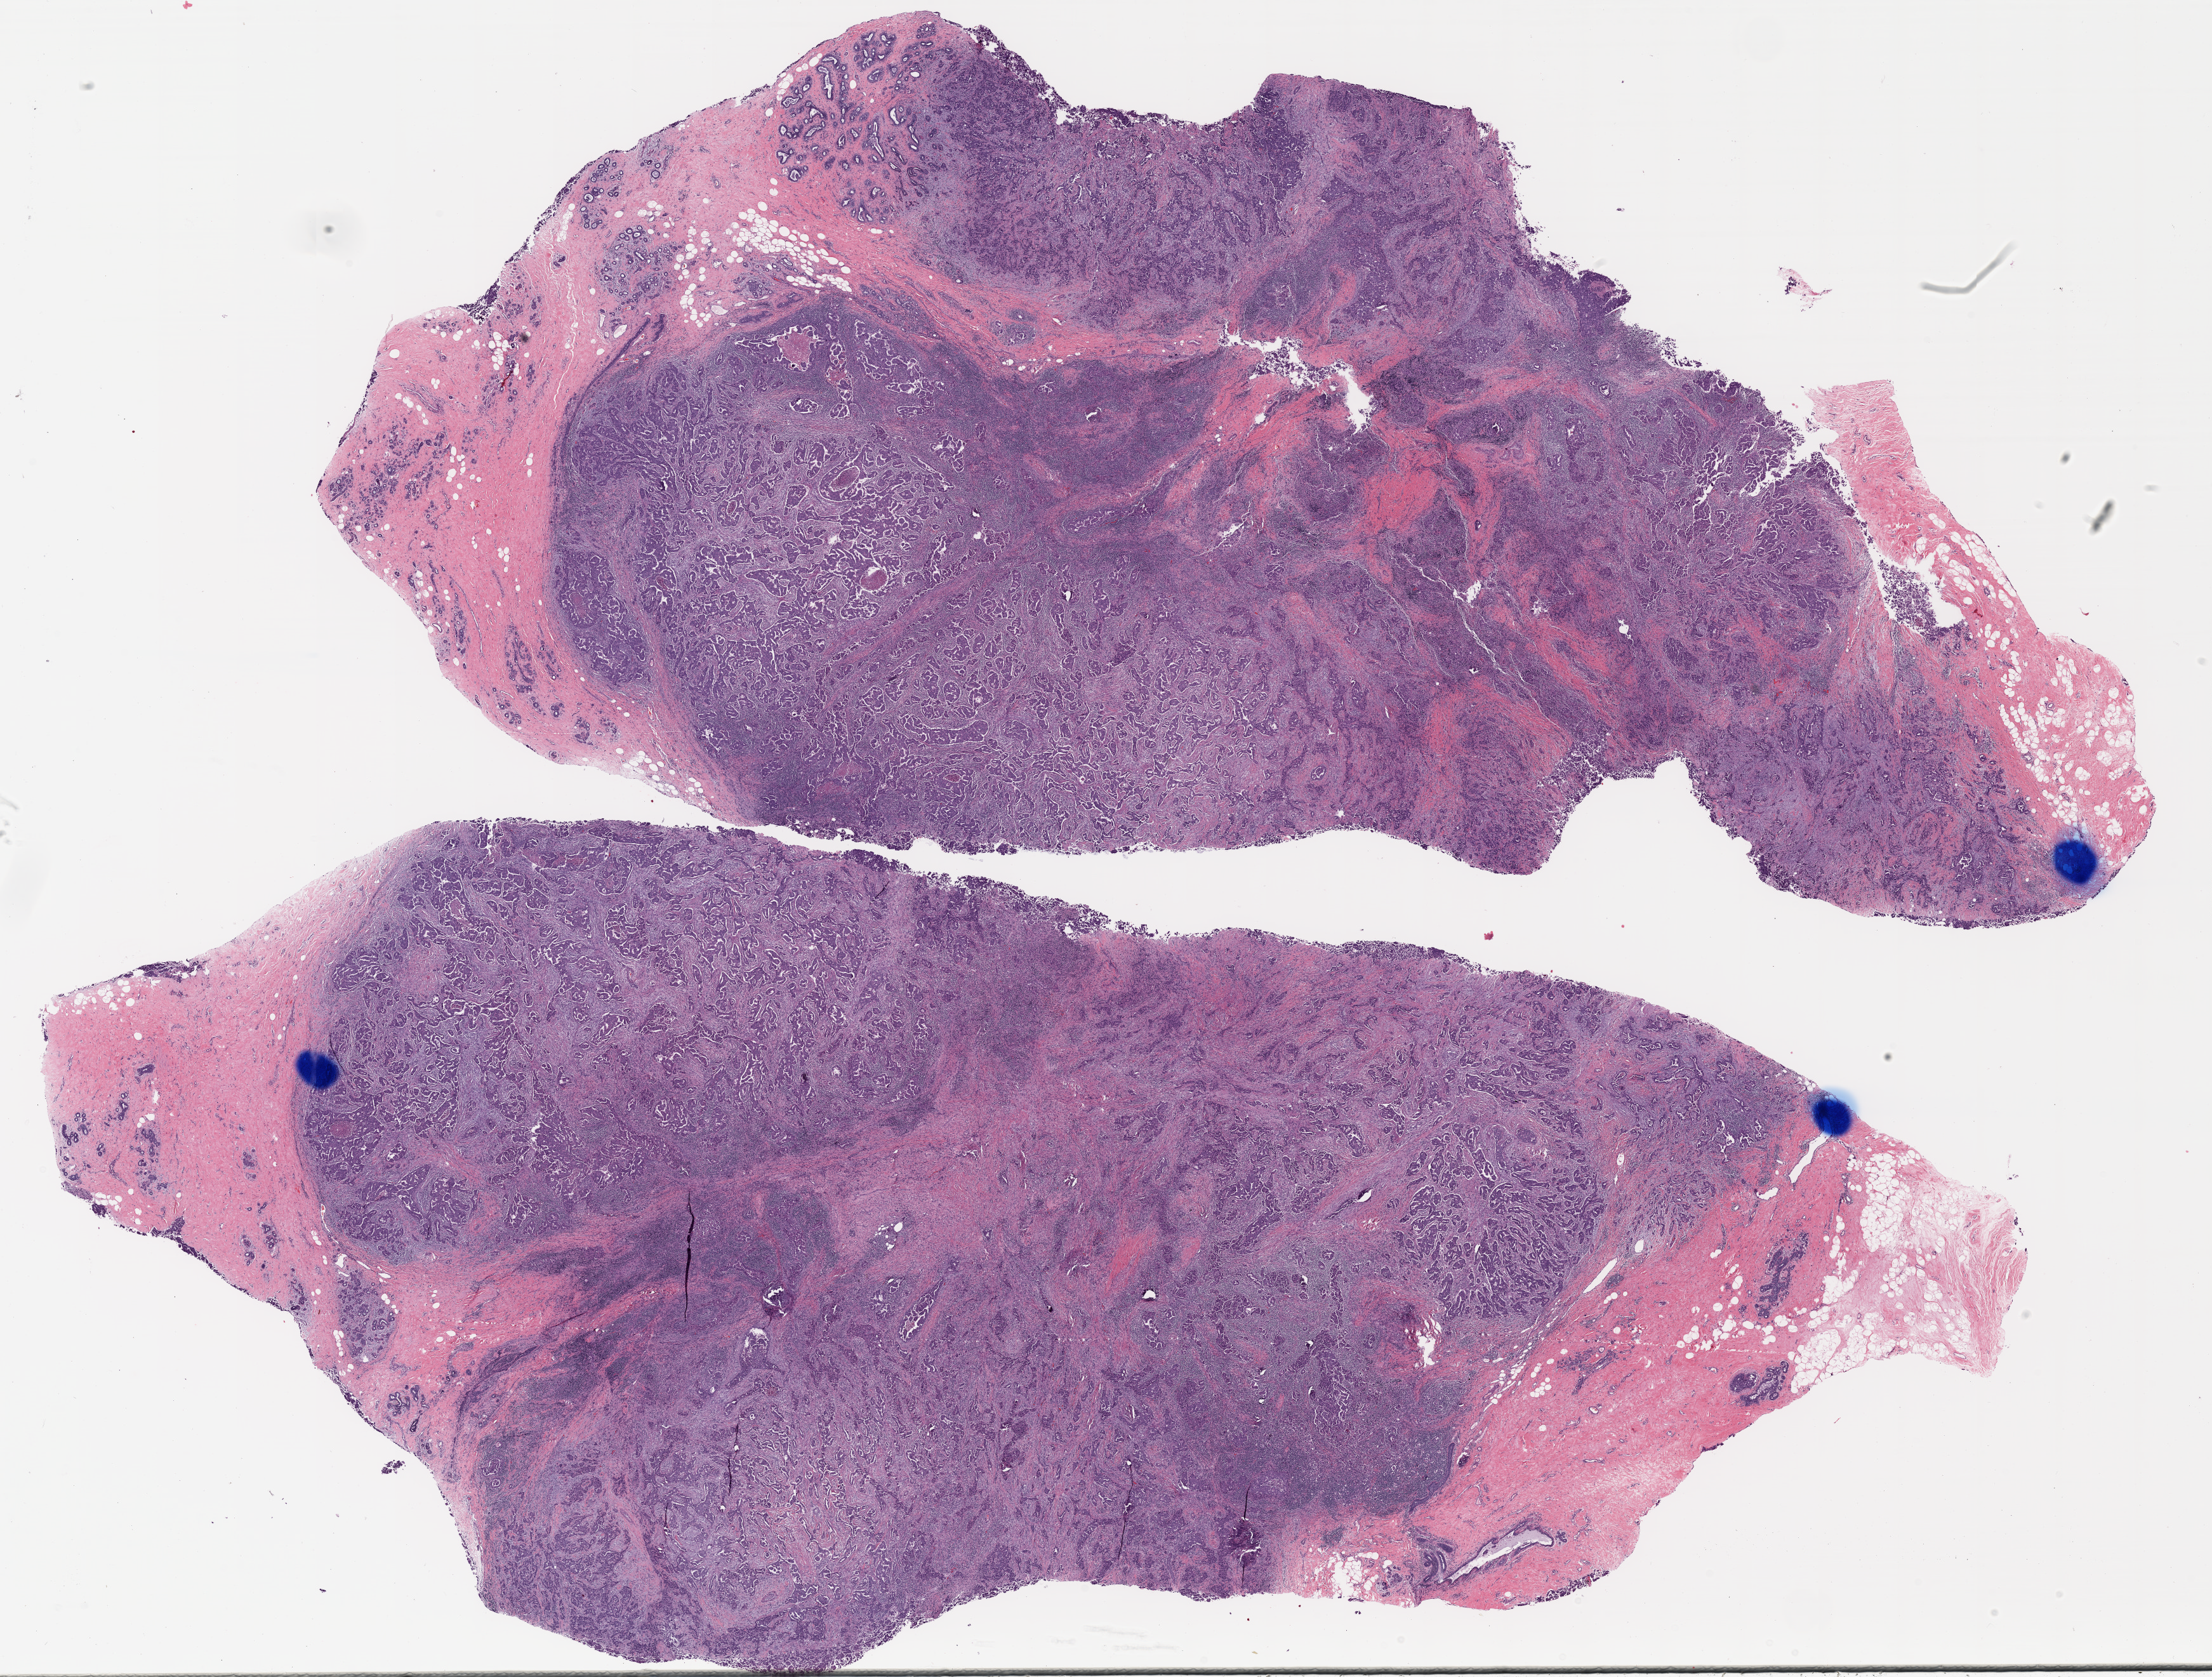
Digitized Hematoxylin and eosin (H&E) stained tissue section (whole slide), shown as a low-resolution overview of the whole scanned area (about 27.8 x 21.1 mm), formalin-fixed paraffin-embedded (FFPE) diagnostic section, breast, primary tumour sample. Female, age 43 years at initial diagnosis.
Laterality: left. Histologic diagnosis: Infiltrating duct carcinoma, NOS. Lymph nodes positive (case pathology): 1 of 16 examined. AJCC pathologic stage: IIA. TNM: T1c N1a M0.